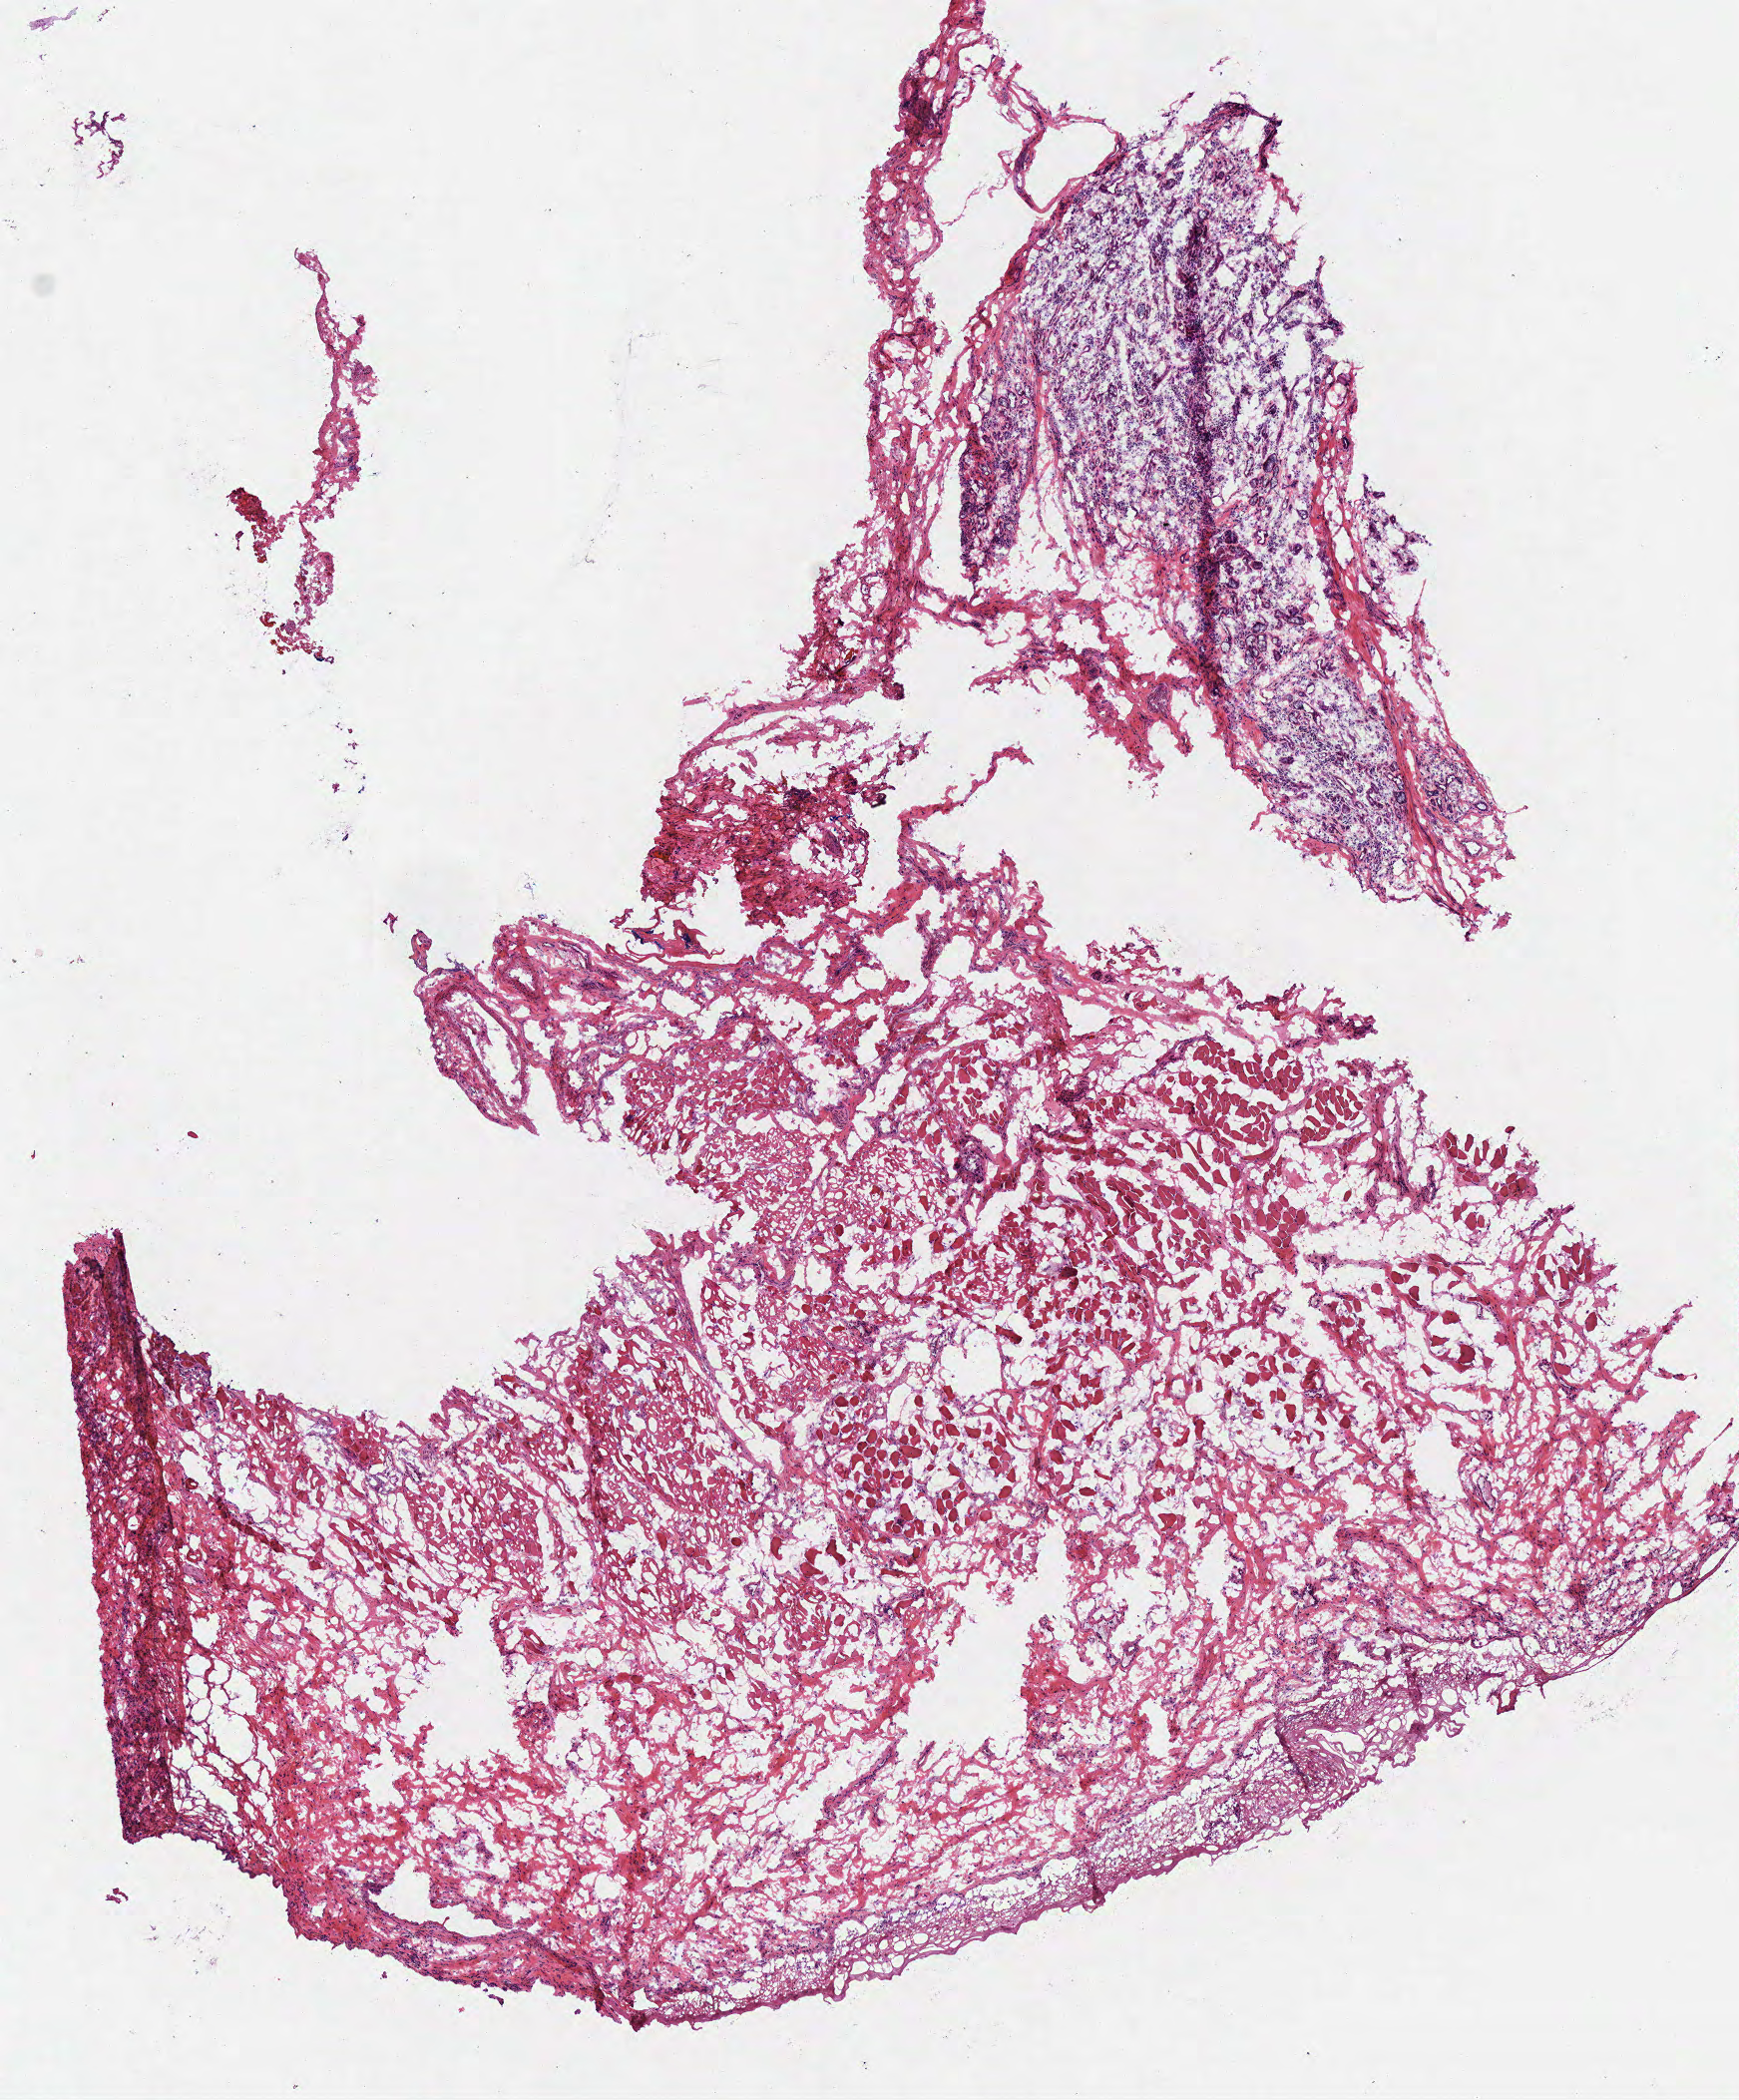
Hematoxylin and eosin (H&E) stained whole-slide image, whole scanned area (about 6.9 x 8.3 mm, slide scanned at 40x) shown as a low-resolution overview. Frozen section from the top of the tissue portion. Sample: solid tissue normal (non-tumour tissue), head and neck. Patient: male, age at initial diagnosis 53 years.
This section: solid tissue normal (non-tumour) sample from the same patient. Patient diagnosis: Squamous cell carcinoma, NOS (overlapping lesion of lip, oral cavity and pharynx).